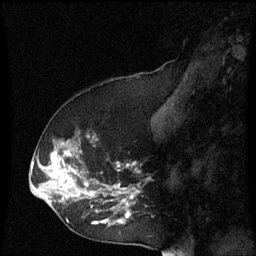
Breast MRI (dynamic contrast-enhanced), one sagittal slice. Position 27 of 60 along the scan axis. Dynamic contrast-enhanced series, image 2 of 3 at this slice position (ordered by acquisition). 1.5 T. TE 4.2 ms, TR 8.9 ms. 2 mm slice thickness. 256 × 256 image matrix. Patient: female, 53 years. From the clinical record (not read from this slice): setting: breast cancer imaged before/during neoadjuvant chemotherapy; receptor status: HR-positive, HER2-negative.
Annotated regions visible in this slice (semi-automatically segmented with operator editing):
- analysis volume of interest (the breast-tissue region the enhancement analysis was run in; not a lesion): bounding box (x1, y1, x2, y2) in pixels: (38, 132, 141, 231)
- tumour enhancement mask (voxels above the 70 % enhancement threshold inside the analysis volume of interest): (48, 142, 139, 225)